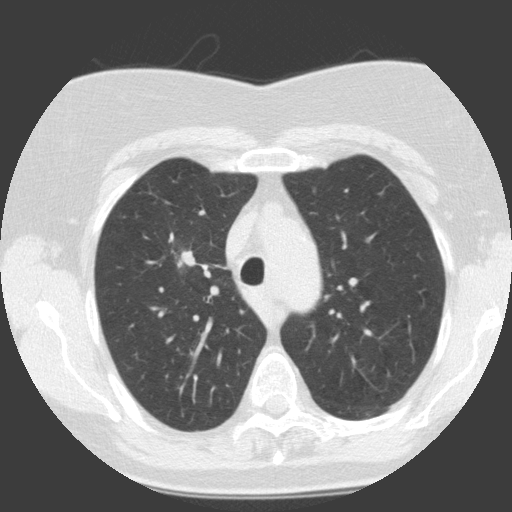
Axial slice from a low-dose chest CT screening exam; first (baseline) screen; lung window (W 1500 / L -600 HU); 2 mm slice thickness; standard (soft-tissue) reconstruction kernel (C); slice 42 of 146 in the series; 512 × 512 image matrix, field of view 300 × 300 mm. Female, age 68 years at enrolment.
Lesion marked by an expert reader, bounding box [x1, y1, x2, y2] px = [156, 232, 210, 282]. Screening reader's record for this exam (one nodule recorded; not confirmed to be the boxed lesion): non-calcified nodule or mass ≥4 mm, right upper lobe, 19 × 12 mm, smooth margins, soft tissue attenuation. Official screen result: positive, change unspecified: nodule(s) >= 4 mm or enlarging nodule(s), mass(es), or other non-specific abnormalities suspicious for lung cancer. Lung cancer was diagnosed 30 days after this screen: squamous cell carcinoma, NOS, right upper lobe, moderately differentiated (G2), stage IA (AJCC 6th edition), 28 mm at pathology.